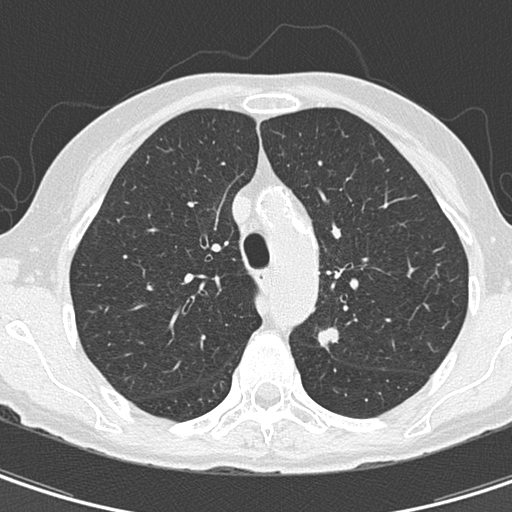
Axial slice from a low-dose chest CT screening exam. Baseline annual screen. Lung window (W 1500 / L -600 HU). 2 mm slice thickness. Slice 47 of 157 in the series. Female participant, aged 67 years at enrolment.
- Lesion marked by an expert reader, box from (x=299, y=318) to (x=356, y=365) px.
- Reader record for this screening exam (exam-level; its link to the box is not recorded): non-calcified nodule or mass ≥4 mm, left upper lobe, 11 × 8 mm, spiculated (stellate) margins, soft tissue attenuation.
- Official screen result: positive, change unspecified: nodule(s) >= 4 mm or enlarging nodule(s), mass(es), or other non-specific abnormalities suspicious for lung cancer.
- Later outcome: lung cancer diagnosed 73 days after this screen — adenocarcinoma, NOS, left upper lobe, poorly differentiated (G3), stage IA (AJCC 6th edition), 13 mm at pathology.